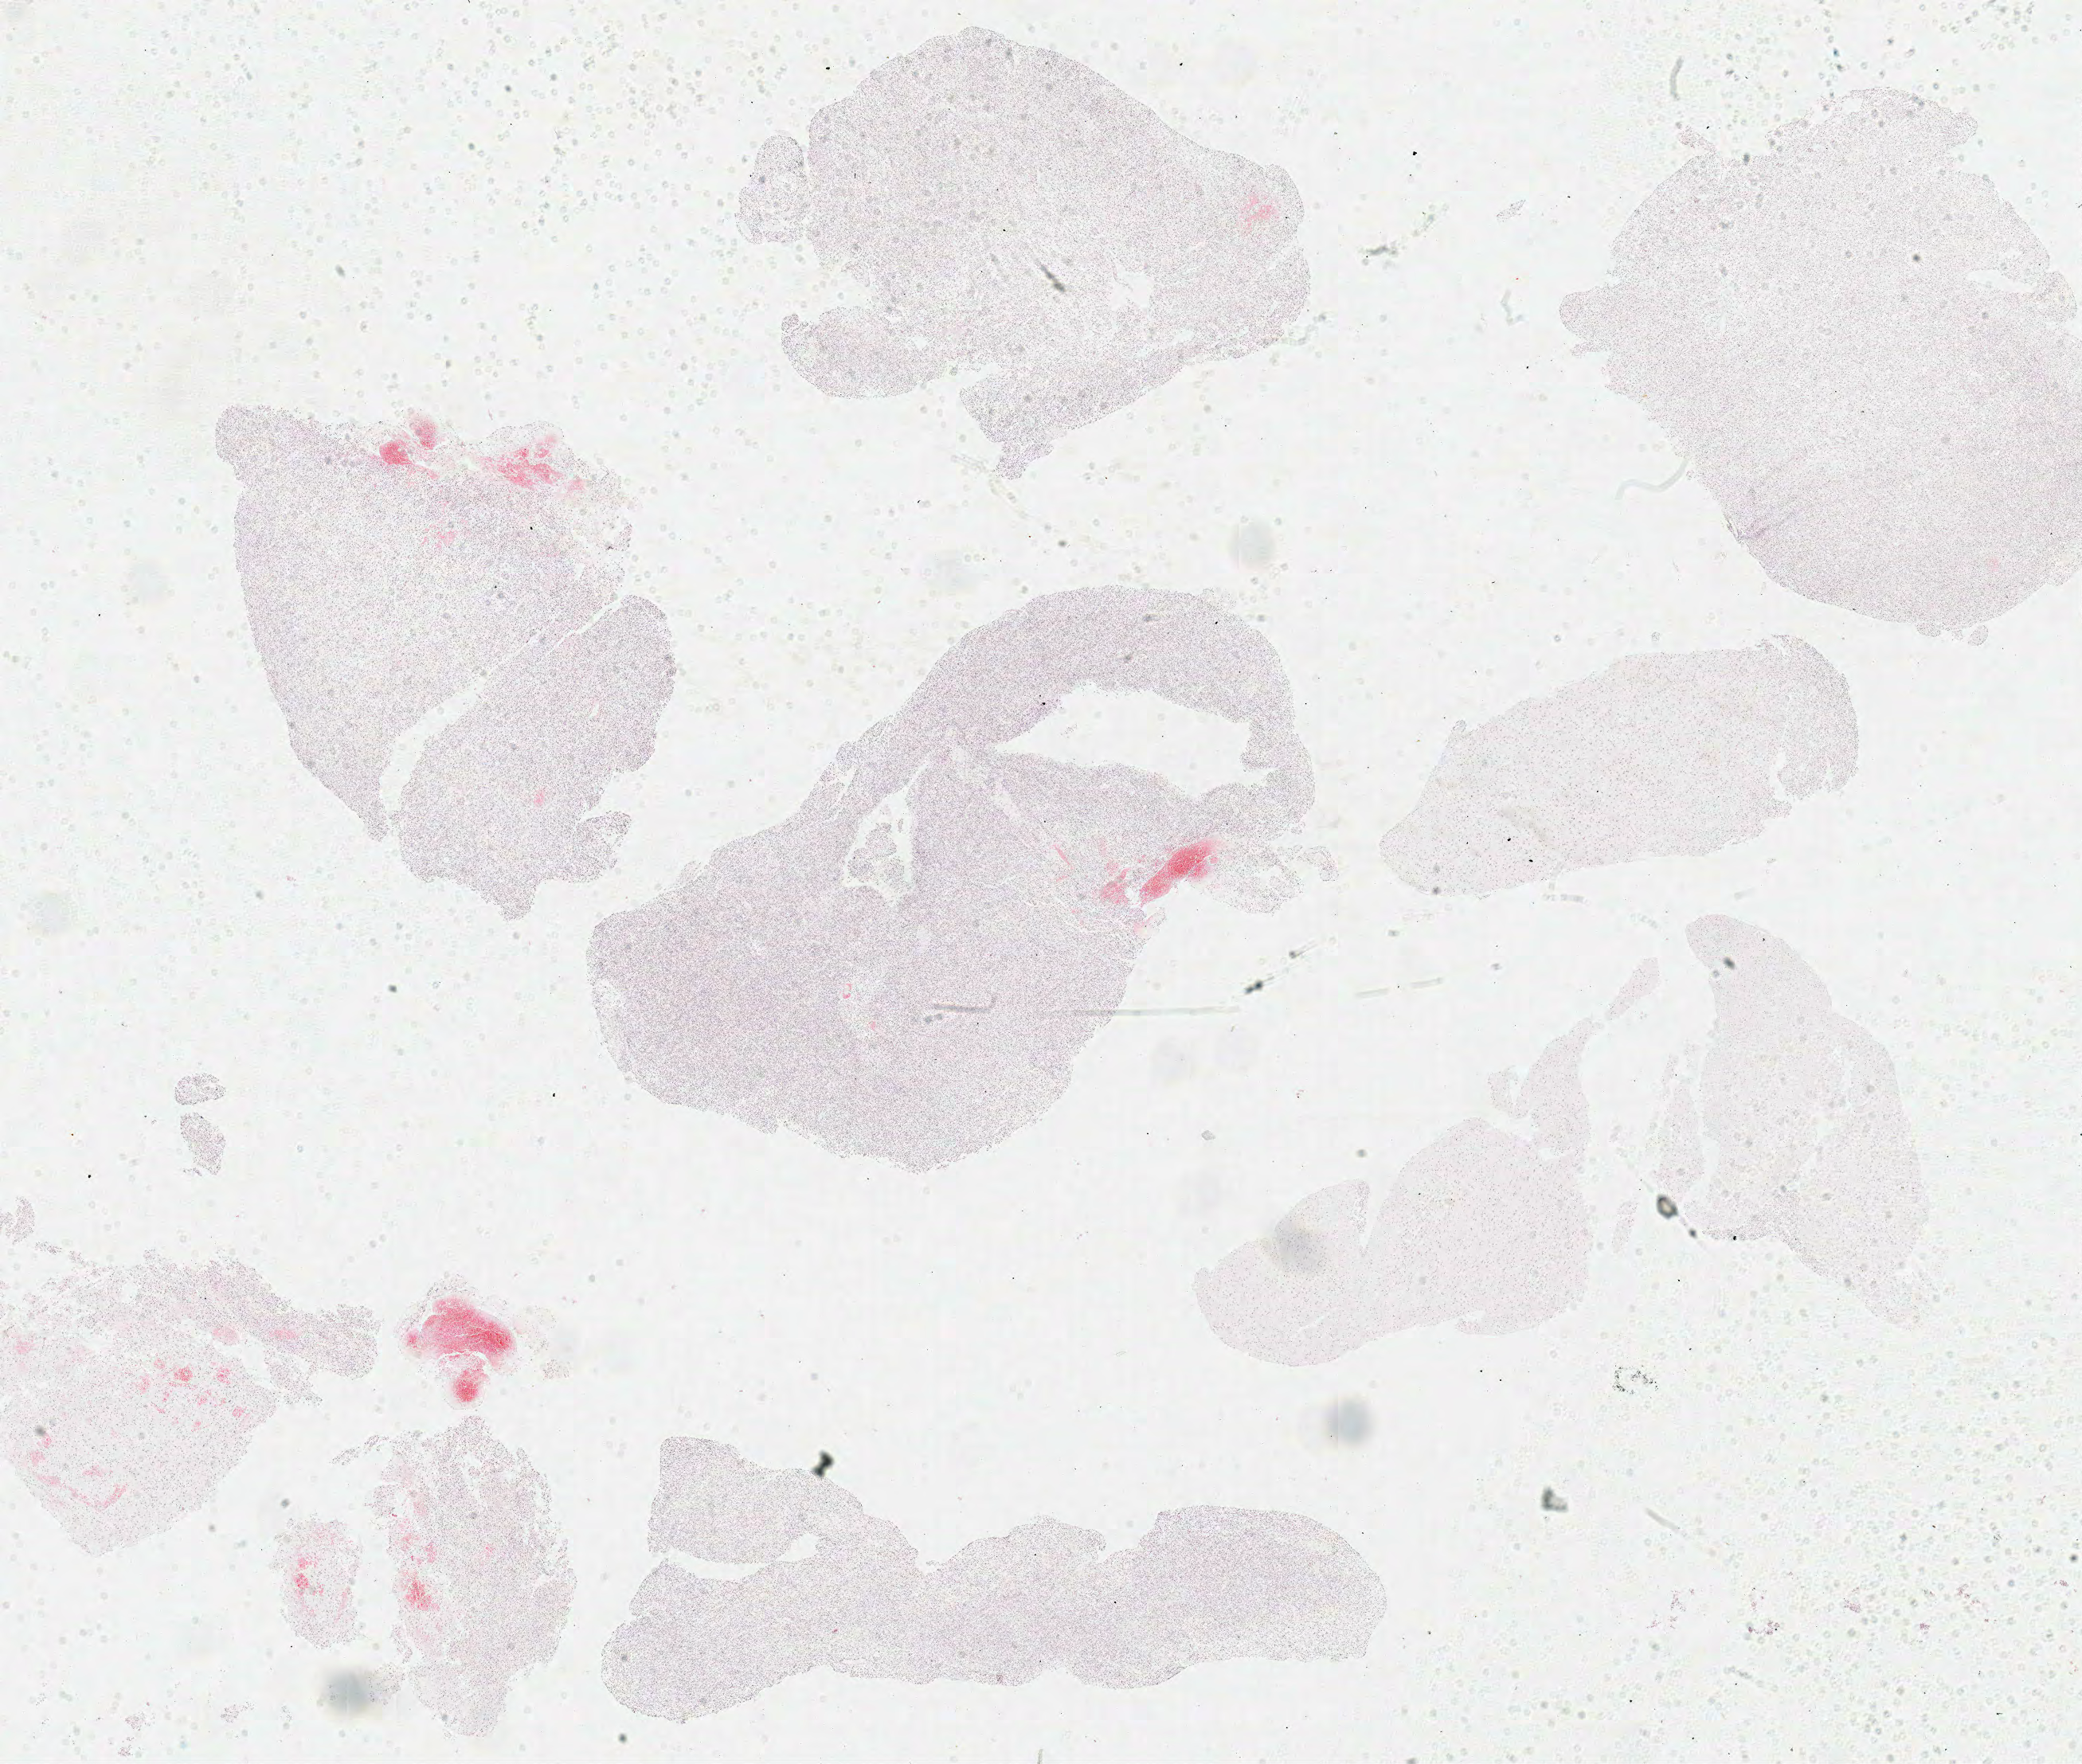
Whole-slide histology image, H&E-stained, a low-resolution overview of the entire scanned area, about 20.6 x 17.4 mm; formalin-fixed paraffin-embedded (FFPE) diagnostic section; sample: primary tumour, brain. Female patient; age at initial diagnosis 48 years.
Pathologic diagnosis: Glioblastoma.